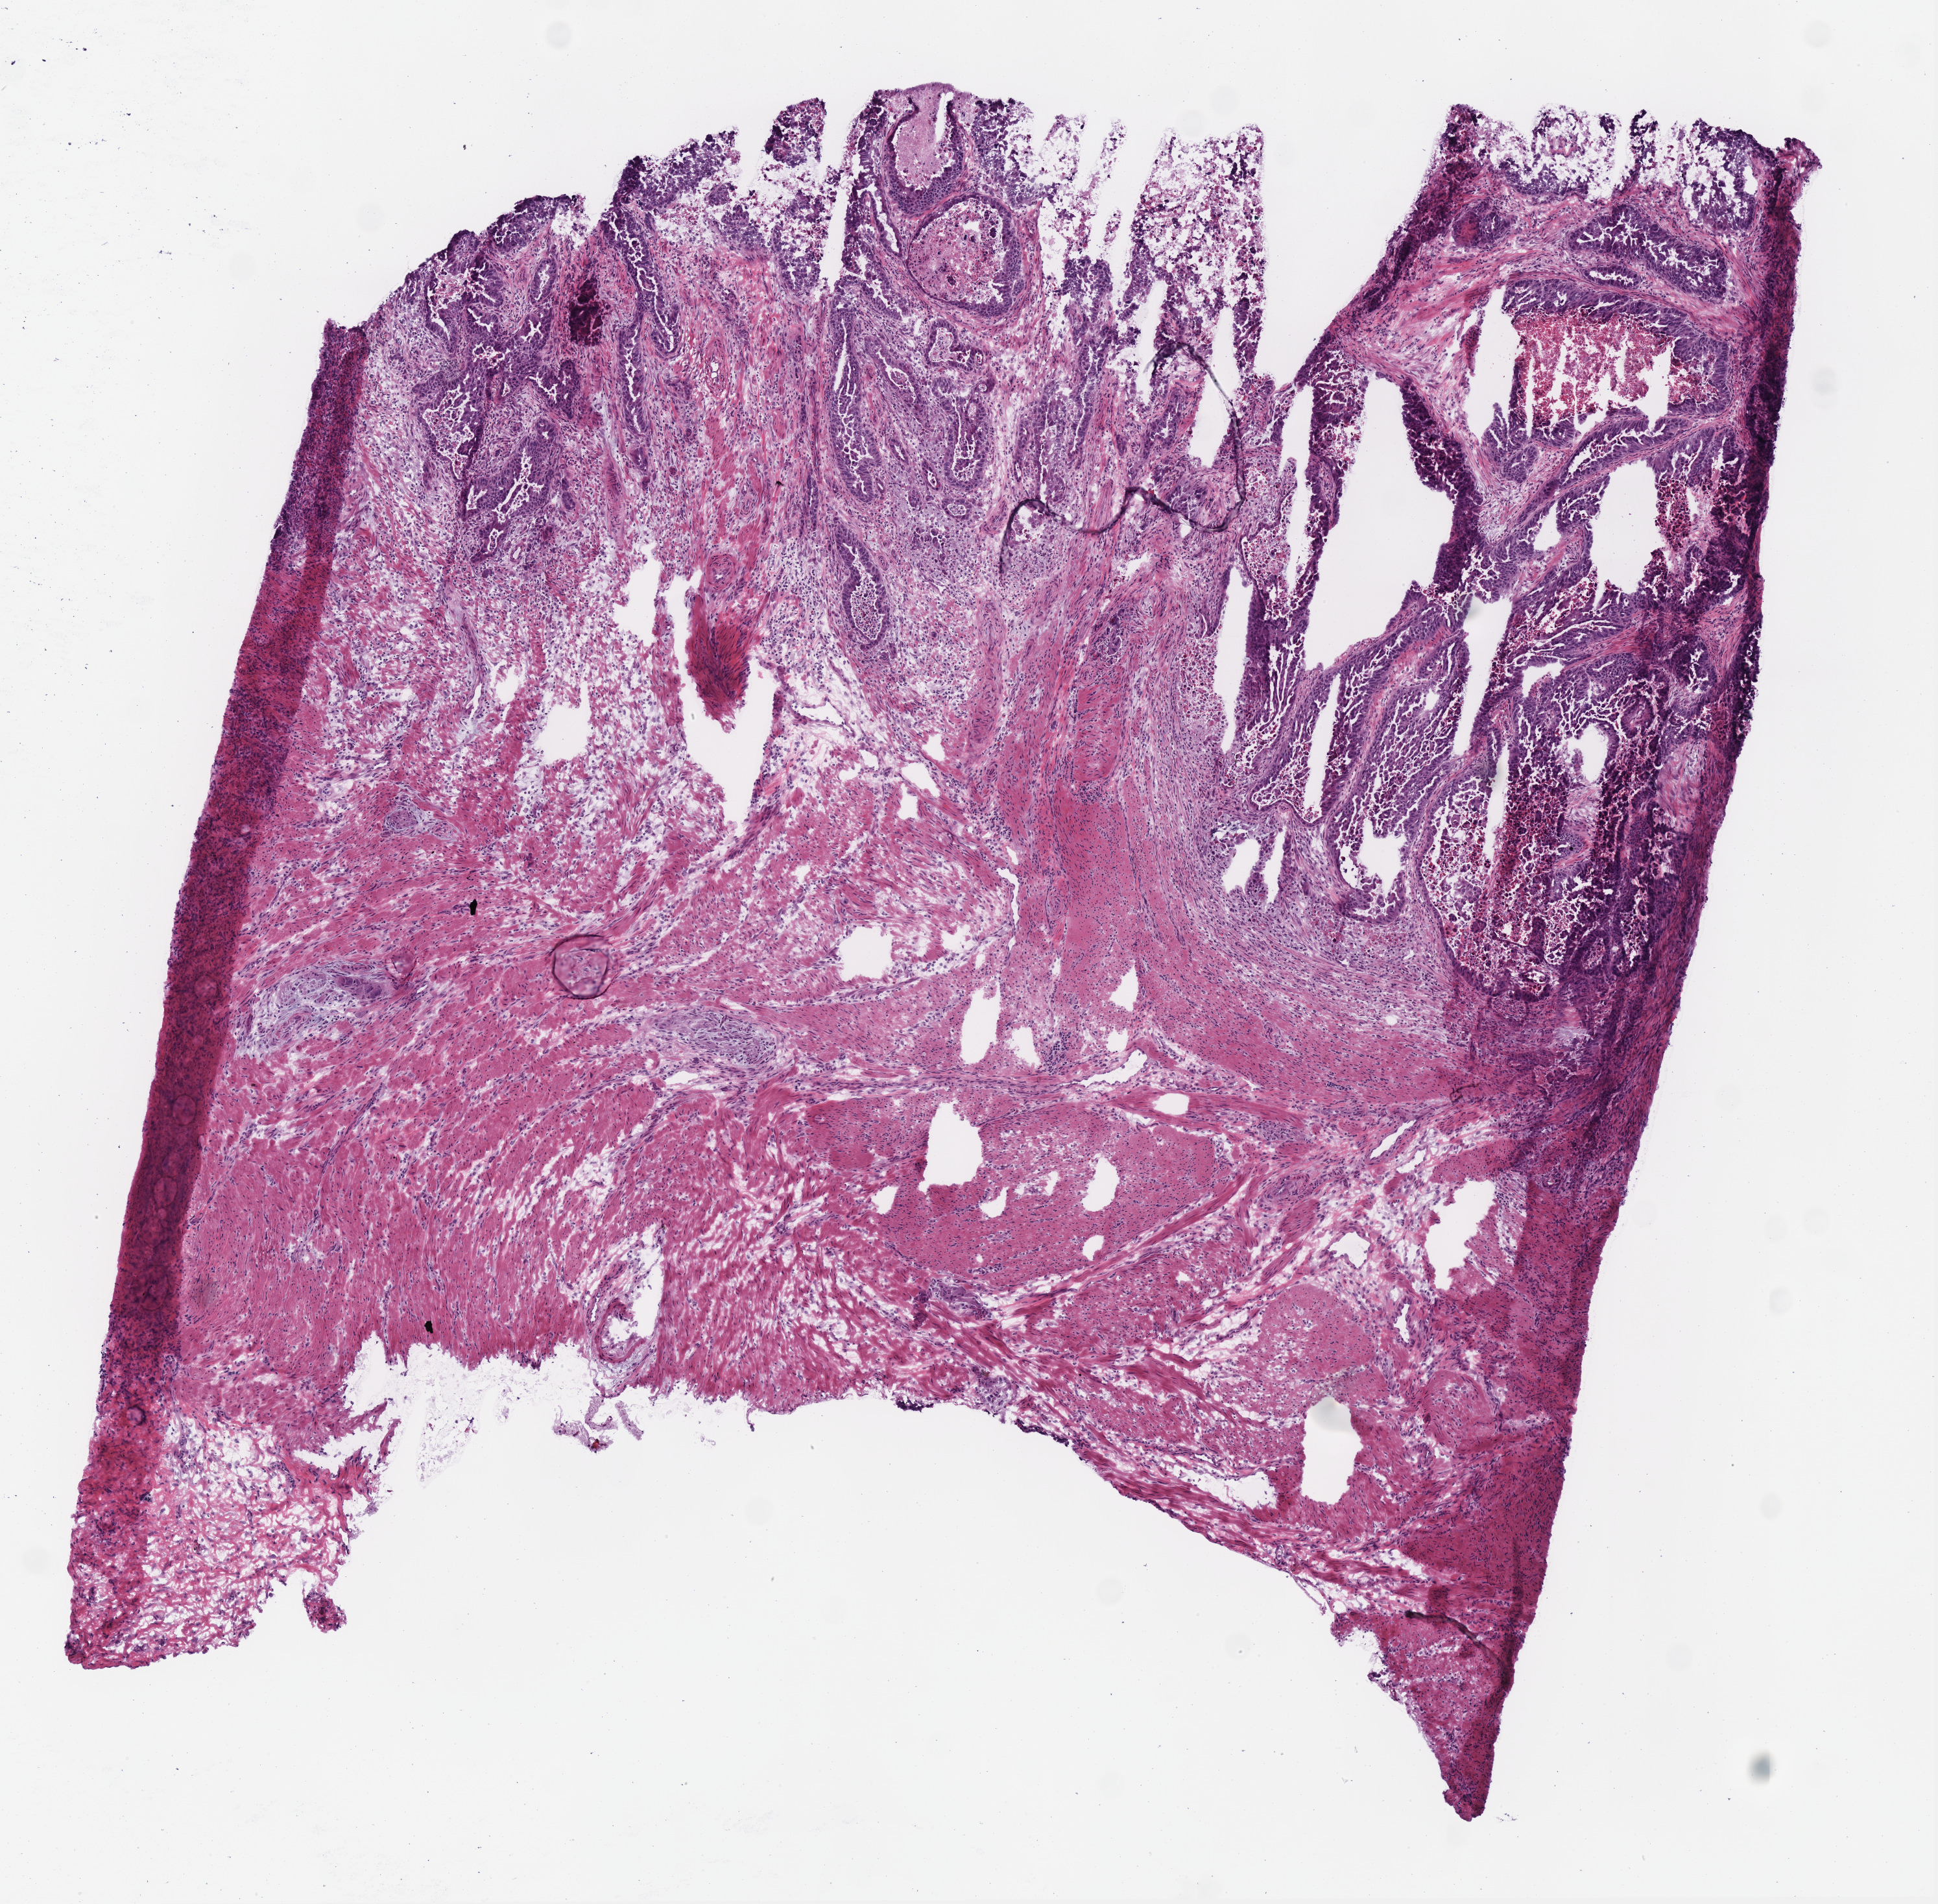
H&E-stained whole-slide image, a low-resolution overview of the entire scanned area, about 5.9 x 5.8 mm (from a 40x scan). Frozen section. Stomach, primary tumour sample. Female, age 71 years at initial diagnosis. Histologic grade: G3 (poorly differentiated). Slide review estimates, as recorded: tumour cells 40%, tumour nuclei 60%, normal cells 50%, stromal cells 0%, necrosis 10%. Inflammatory infiltration, as recorded: lymphocyte infiltration 10%, monocyte infiltration 10%, neutrophil infiltration 15%.
* AJCC pathologic stage: IIB (7th edition)
* diagnosis: Adenocarcinoma, intestinal type (gastric antrum)